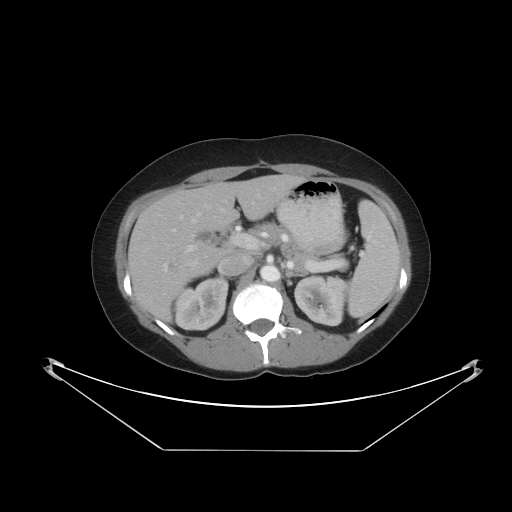
Contrast-enhanced abdominal CT, one axial slice; position 26 of 48 along the scan axis; reconstruction kernel STANDARD; 120 kVp; intravenous contrast given; soft-tissue window (W 400 / L 40 HU); 512 × 512 image matrix, field of view 482 × 482 mm. Female patient, age 38 years. From the clinical record (not read from this slice): diagnosis: colorectal cancer liver metastases, imaged before liver resection; multiple liver metastases: yes; largest metastasis: 2.5 cm; disease in both lobes: no.
Annotated regions visible in this slice (manually delineated by an expert):
- hepatic veins: bounding box [x1, y1, x2, y2] px = [192, 213, 201, 223]
- liver: [128, 175, 300, 321]
- planned liver remnant (the part of the liver to remain after resection): [163, 175, 301, 232]
- portal vein (with intrahepatic branches): [173, 188, 275, 265]
- liver metastasis: [166, 262, 181, 274]